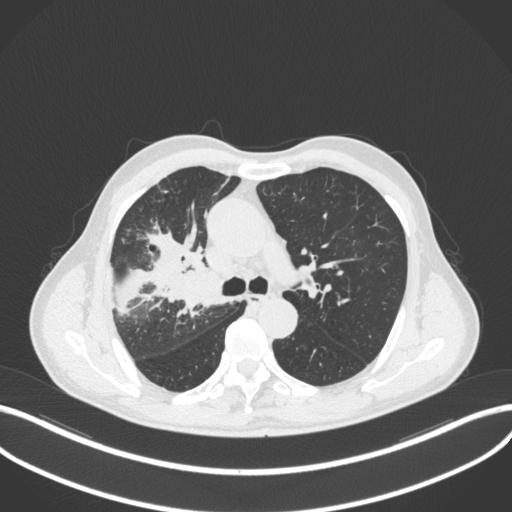
Chest CT, one axial slice. Position 321 of 490 along the scan axis. Reconstruction kernel B31f. 120 kVp. Lung window (W 1500 / L -600 HU). 1 mm slice thickness. 512 × 512 image matrix. Patient: male, 69 years. Case-level facts recorded for this patient, not image findings: clinical TNM (as recorded): T2a N0 M0.
Structures marked on this image (rectangle marked by the reading radiologist):
- lung tumour (recorded histology: adenocarcinoma): bounding box [x1, y1, x2, y2] px = [171, 269, 215, 317]